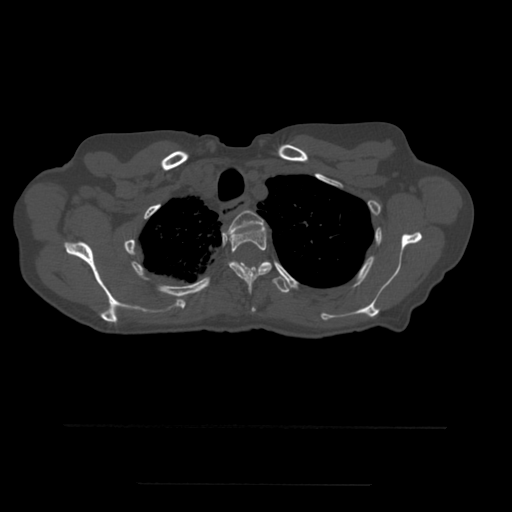
CT including the spine, one axial slice; position 420 of 544 along the scan axis; bone window (W 1800 / L 400 HU); 1.25 mm slice thickness; 512 × 512 image matrix, field of view 350 × 350 mm. Patient age 58 years. Case-level facts recorded for this patient, not image findings: primary cancer: lung.
Structures marked on this image (semi-automatically segmented with operator editing):
- T2 vertebra: bounding box [x1, y1, x2, y2] px = [223, 210, 266, 239]
- T3 vertebra: [229, 227, 272, 312]
- T4 vertebra: [239, 263, 292, 293]